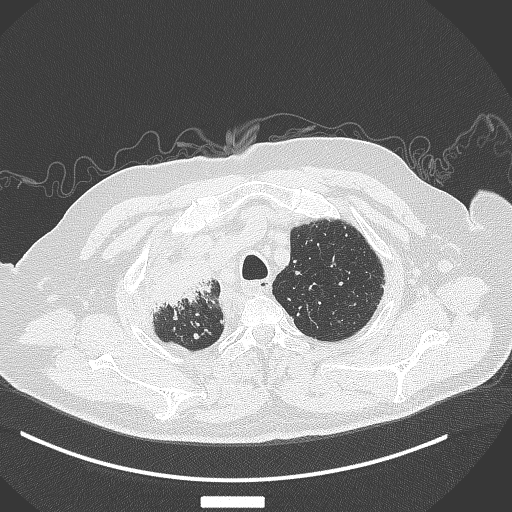
Chest CT, one axial slice; 120 kVp; lung window (W 1500 / L -600 HU); 1 mm slice thickness; 512 × 512 image matrix, field of view 400 × 400 mm. Patient: male, 69 years. From the clinical record (not read from this slice): clinical TNM (as recorded): T4 N3 M1.
Annotated regions visible in this slice (bounding box drawn by a radiologist):
- lung tumour (recorded histology: adenocarcinoma): bounding box <148,256,226,318> (left, top, right, bottom; pixels)